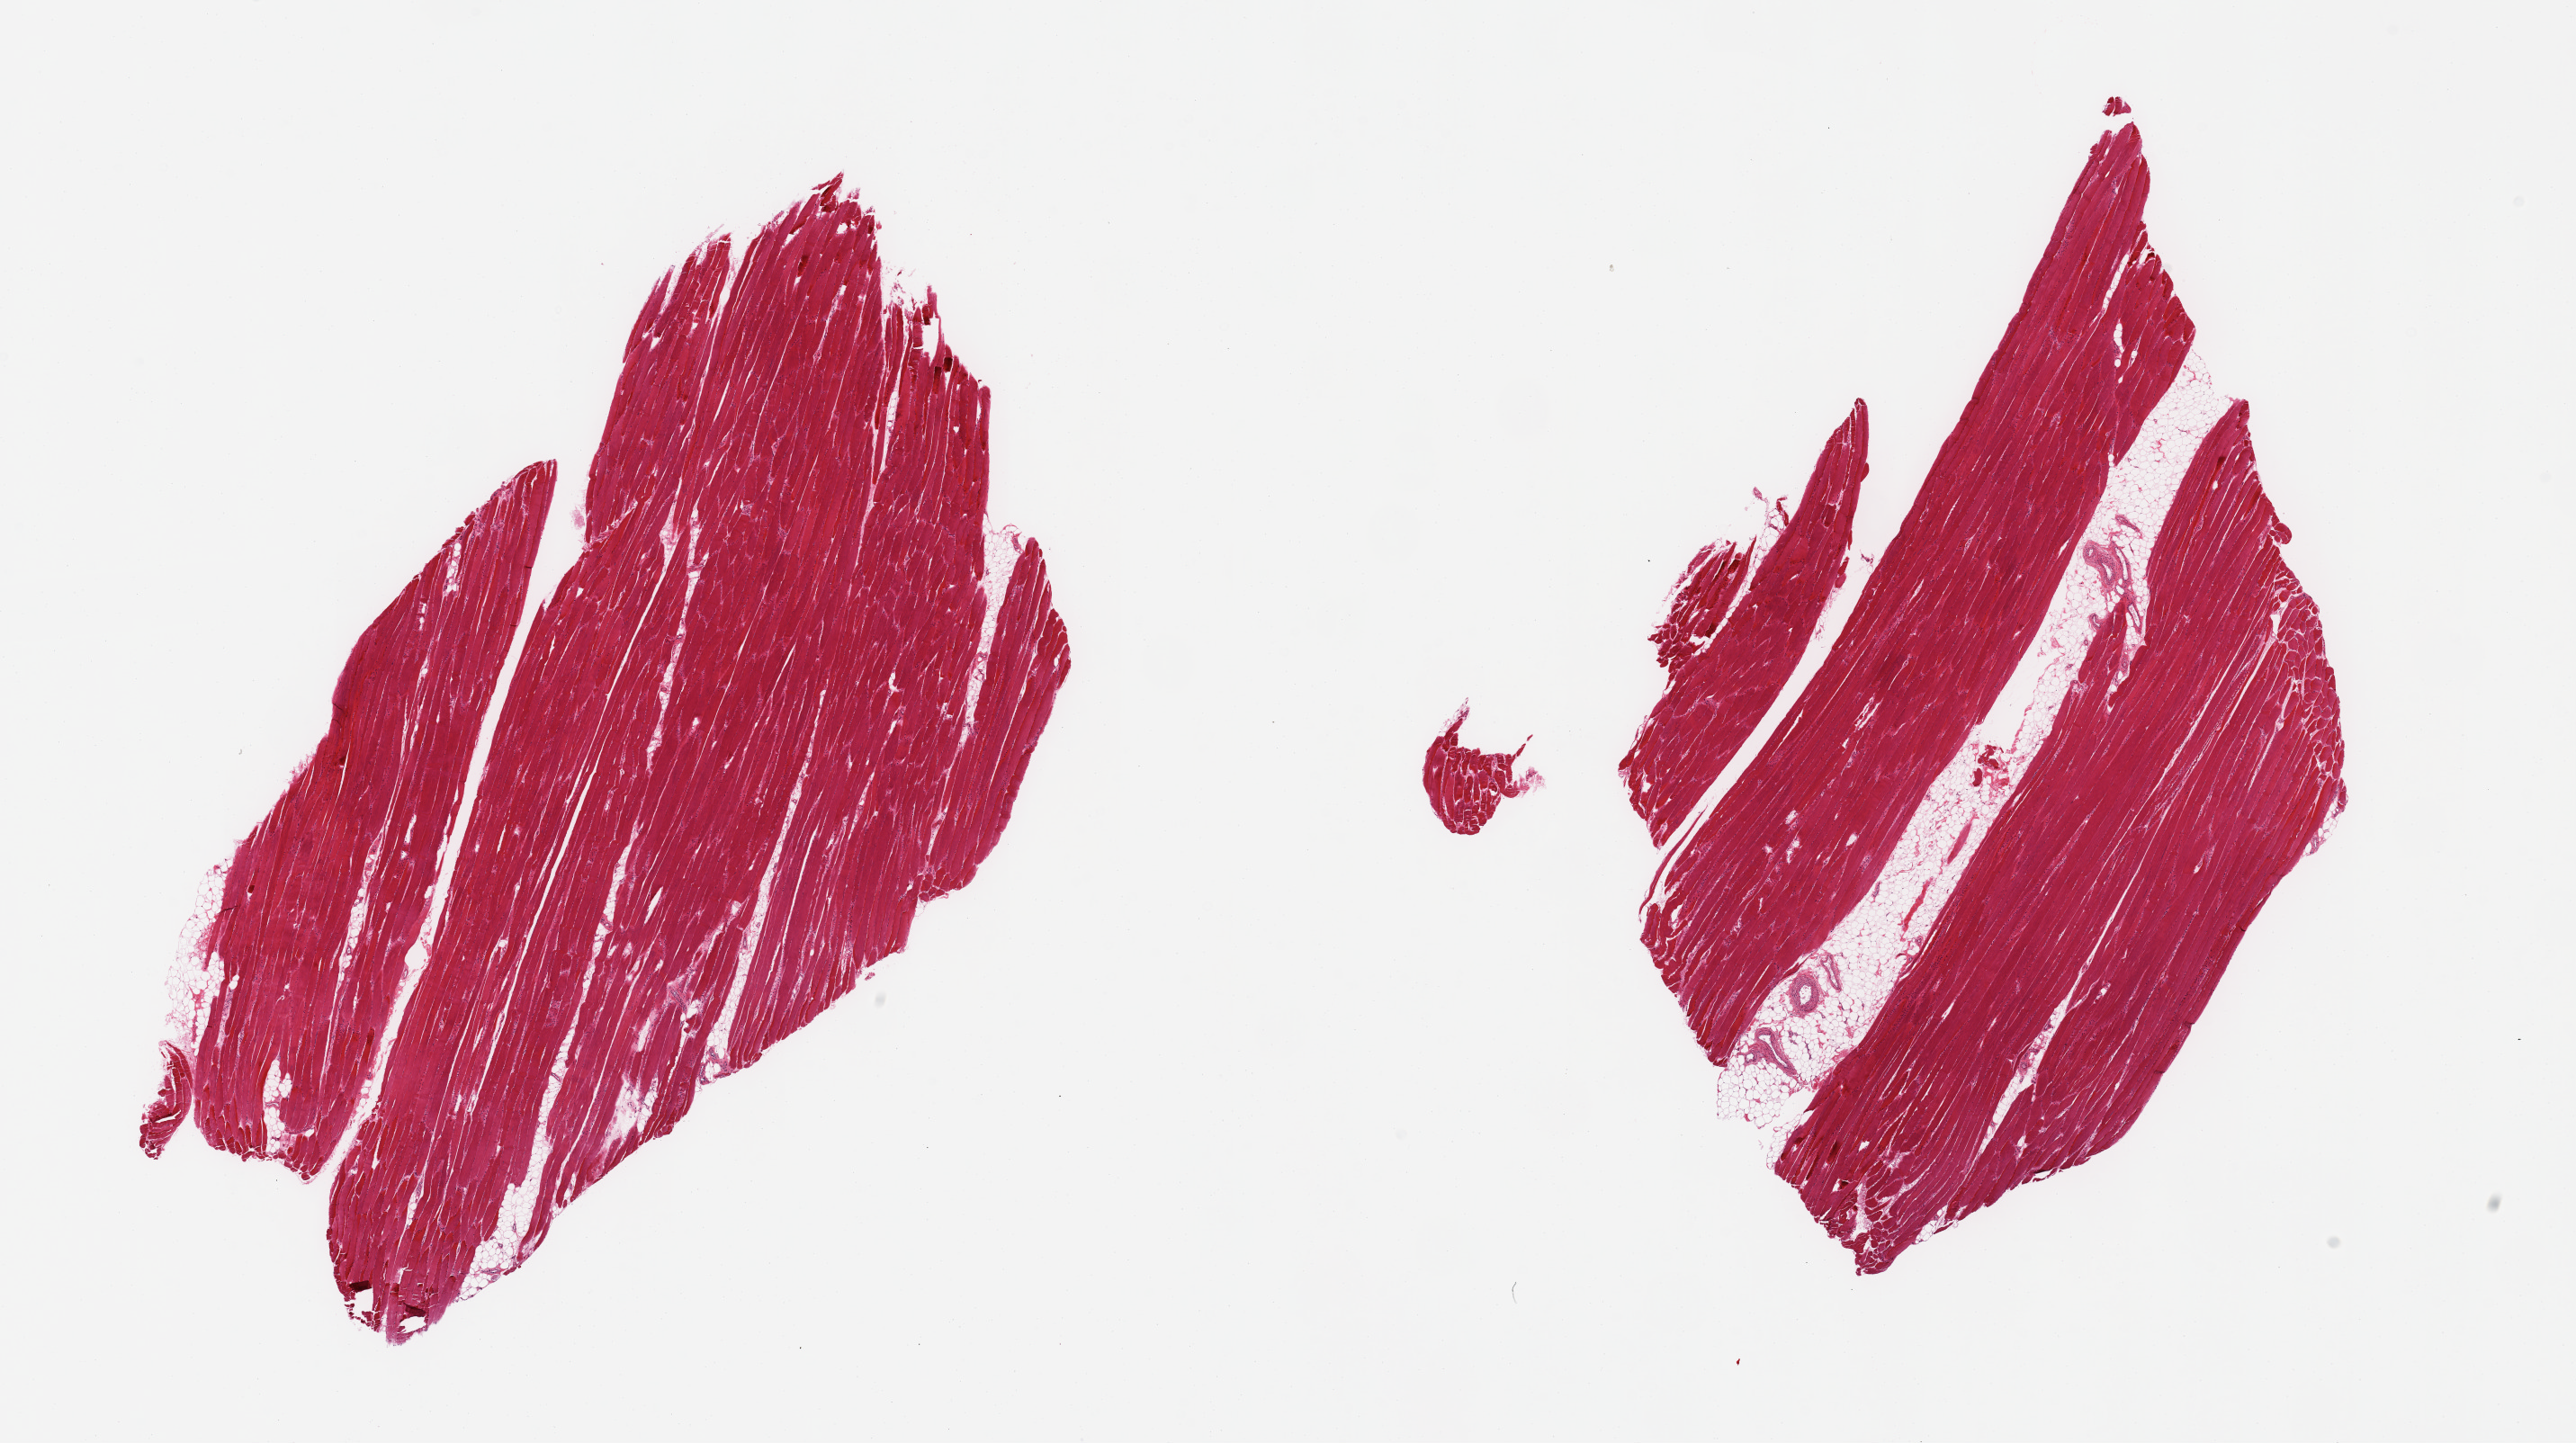
H&E whole-slide image — a low-resolution overview of the entire scanned area, about 22.6 x 12.7 mm (acquisition: 20x scan); PAXgene-fixed, paraffin-embedded tissue; sampled site (target tissue): skeletal muscle; donor tissue sample.
* pathologist's review note for this sample: 2 pieces, ~10% interstitial fat/vascalar elements